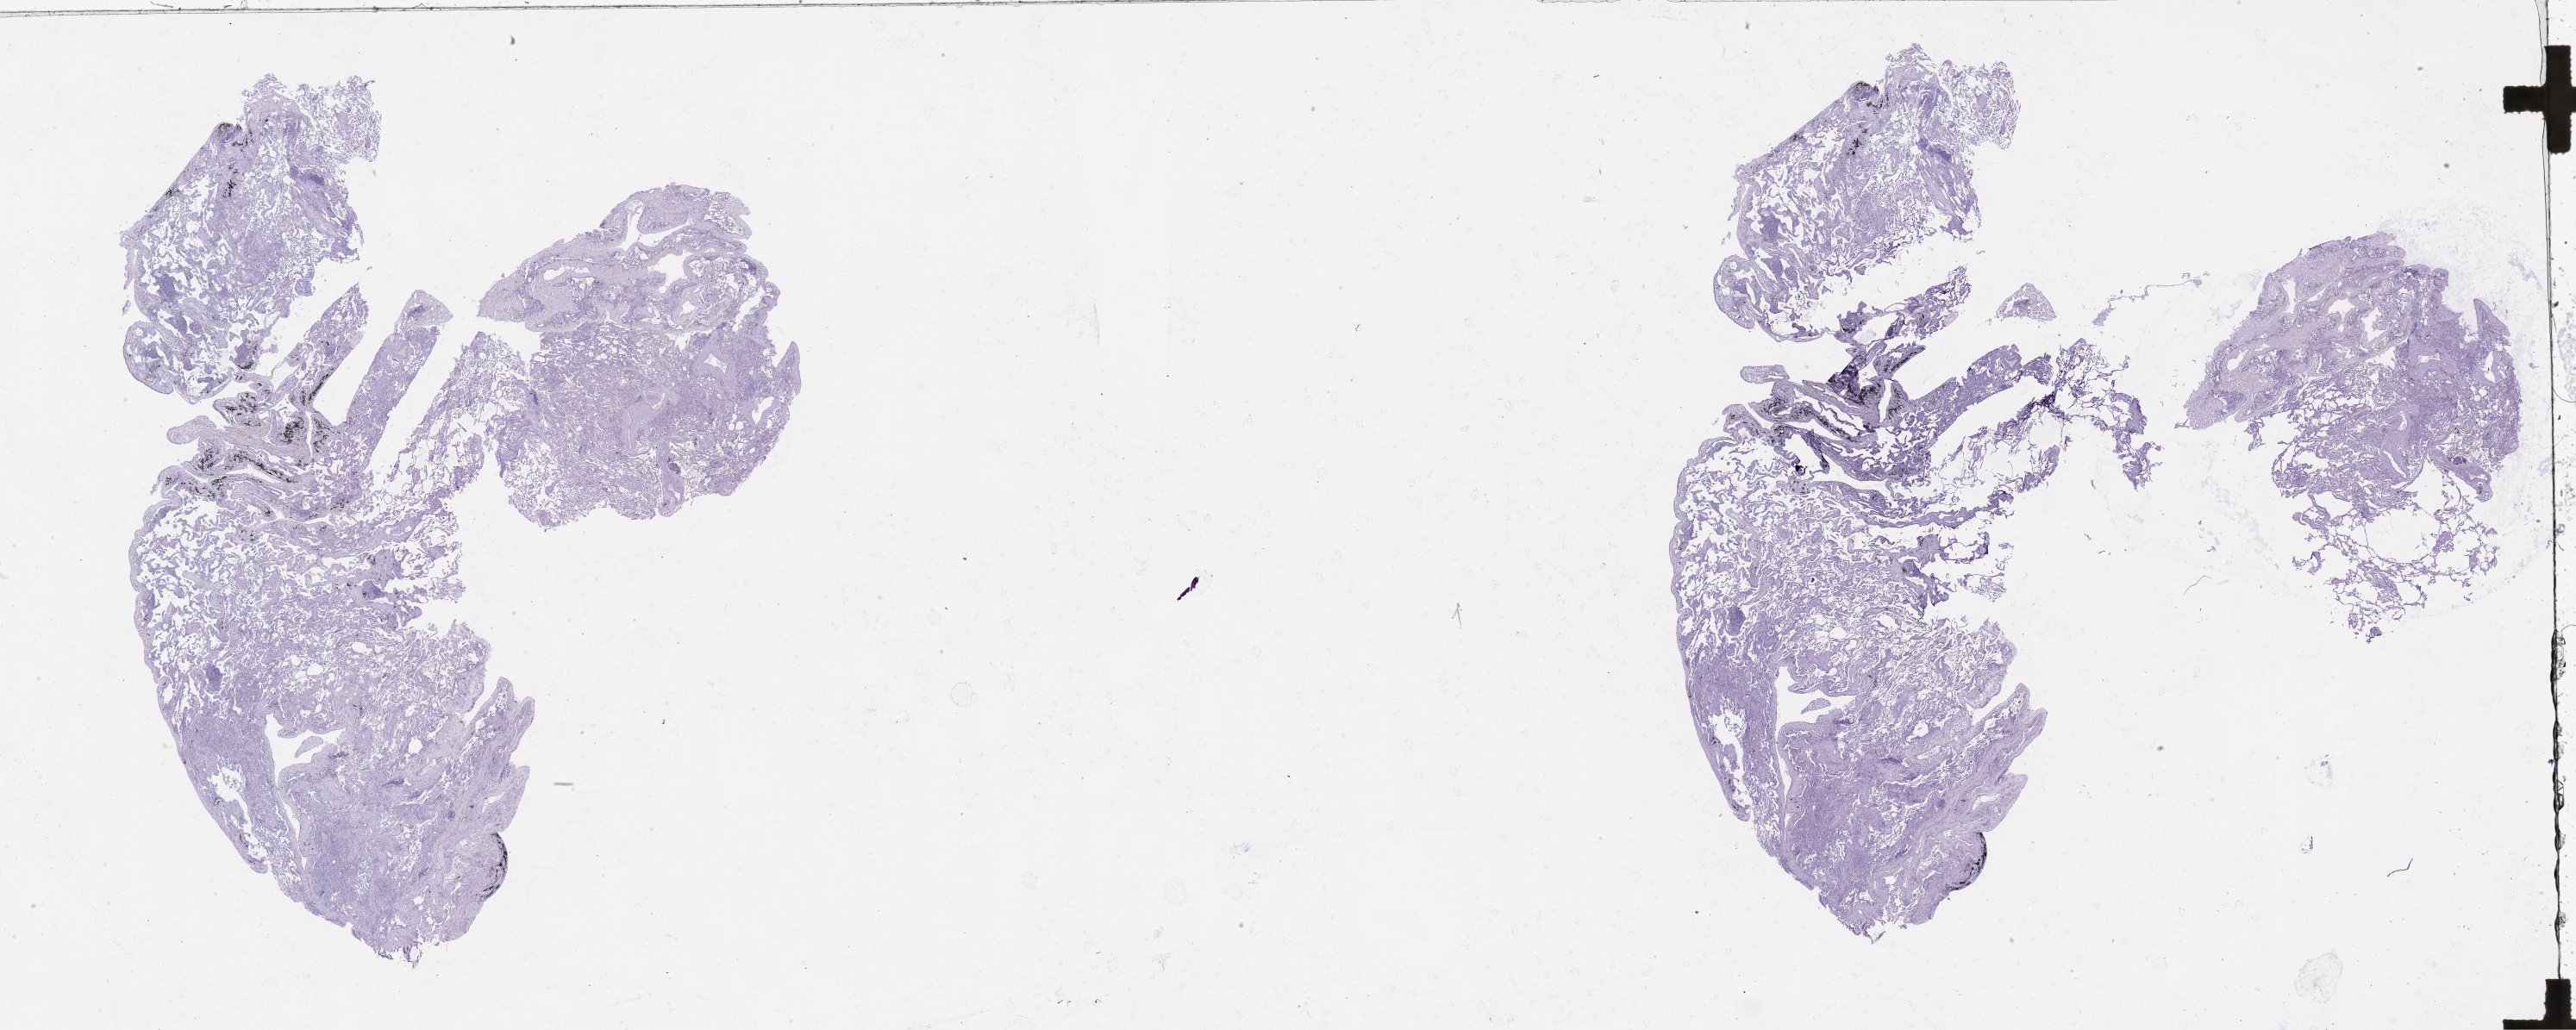
Digitized Hematoxylin and eosin (H&E) stained tissue section (whole slide), shown as a low-resolution overview of the whole scanned area (about 48.1 x 19.2 mm), normal (non-tumour) tissue sample, lung. 68-year-old male patient.
This section: normal (non-tumour) tissue from the same patient. Patient diagnosis (cohort enrolment): squamous cell carcinoma (lung).